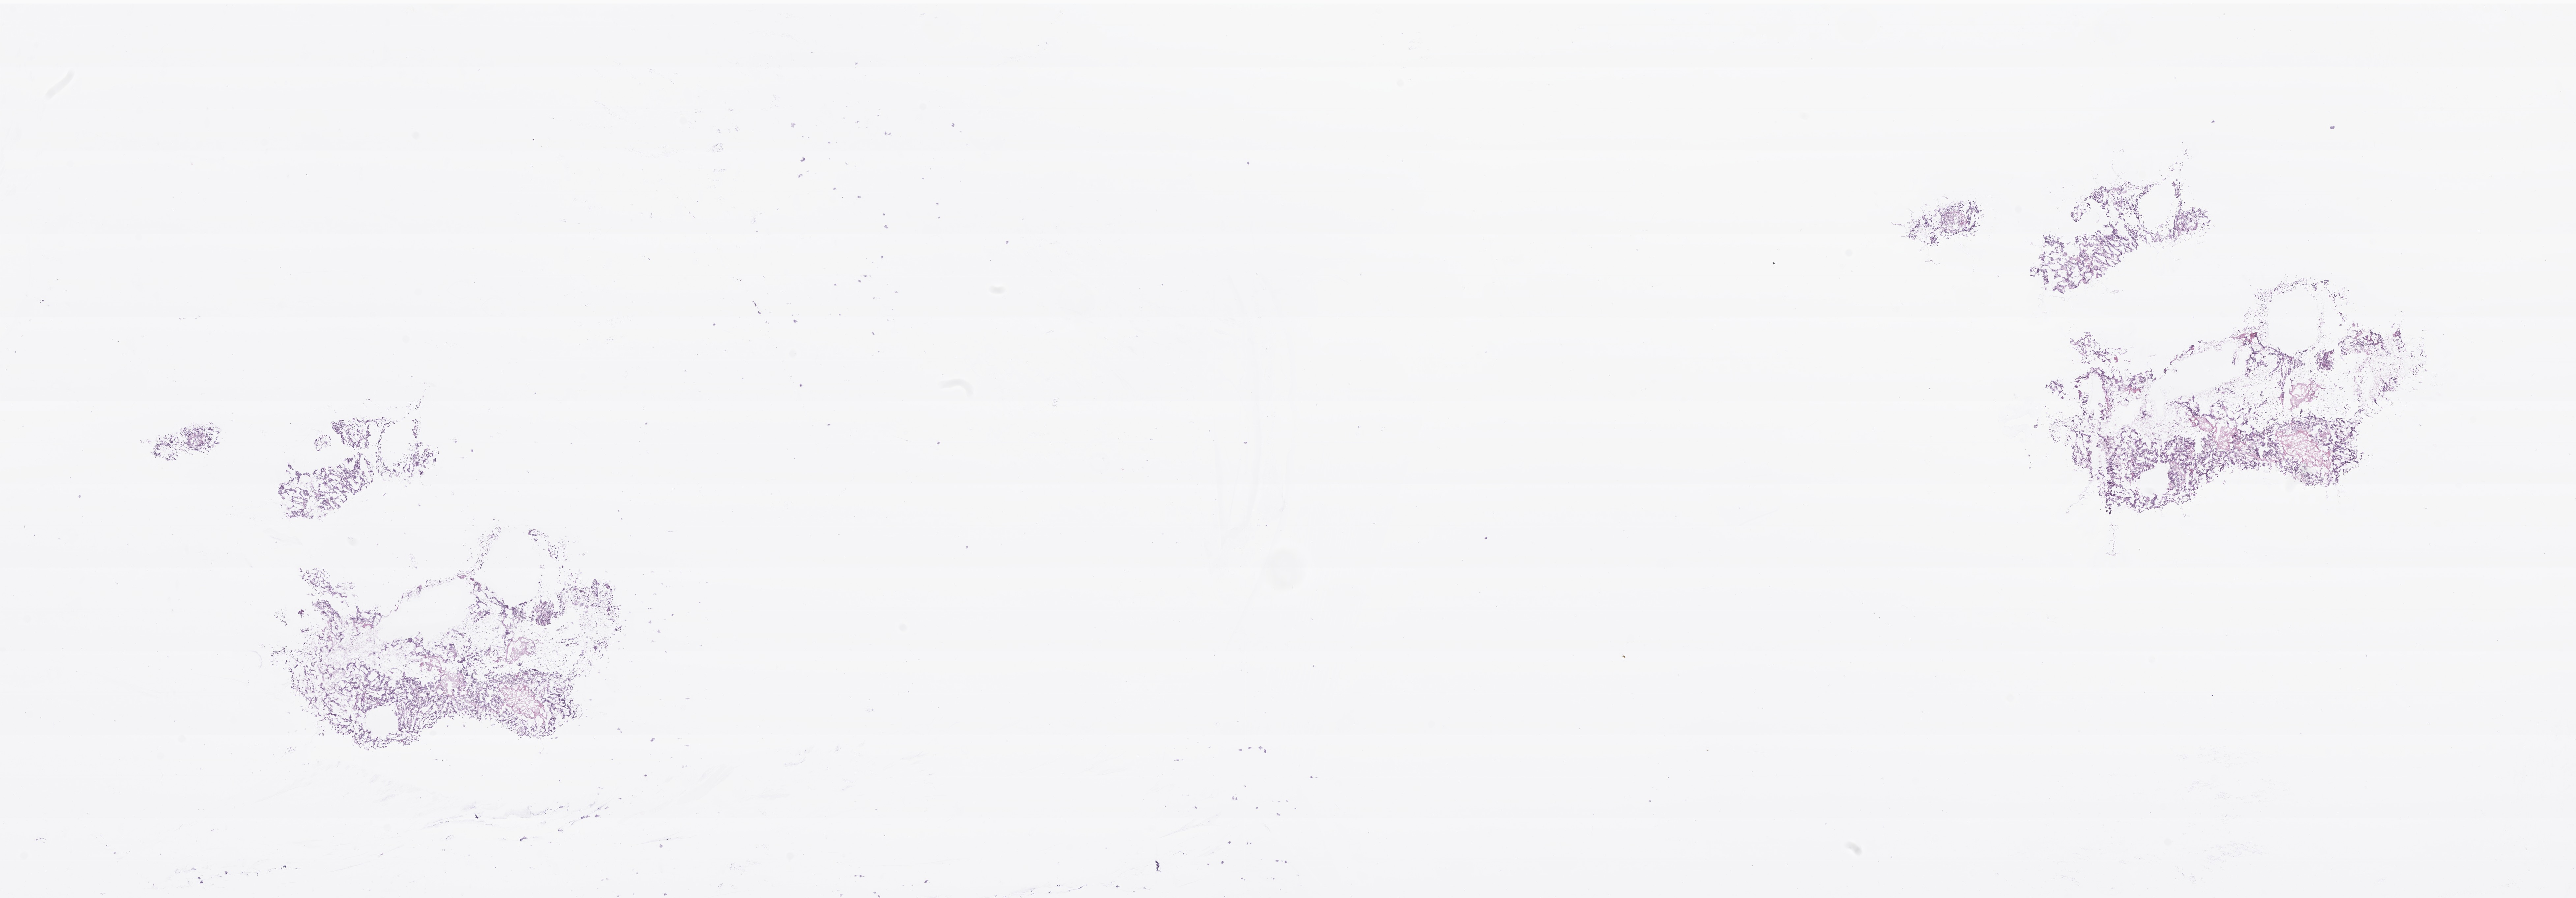
Digitized hematoxylin and eosin (H&E)-stained section of tumor tissue from the brain, a low-resolution overview of the entire scanned area, about 32.9 x 11.5 mm, cryosection (OCT / tissue freezing medium). Patient female; age 38 months (3 years 2 months).
Recorded diagnosis: Neoplasm, uncertain whether benign or malignant.